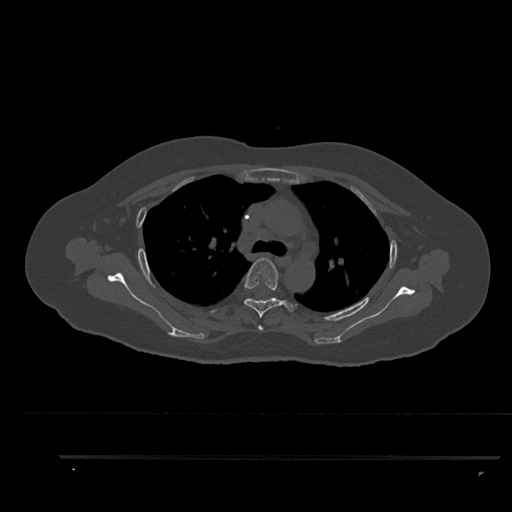
CT including the spine, one axial slice; slice 641 of 797 in the series (ordered by position); bone window (W 1800 / L 400 HU); 512 × 512 image matrix. Patient: female, 44 years. From the clinical record (not read from this slice): primary cancer: renal; vertebrae with lytic lesions (as recorded): L1.
Outlined on this slice (semi-automatically segmented with operator editing):
- T3 vertebra: bounding box (x1, y1, x2, y2) in pixels: (258, 325, 264, 331)
- T4 vertebra: (244, 258, 294, 319)